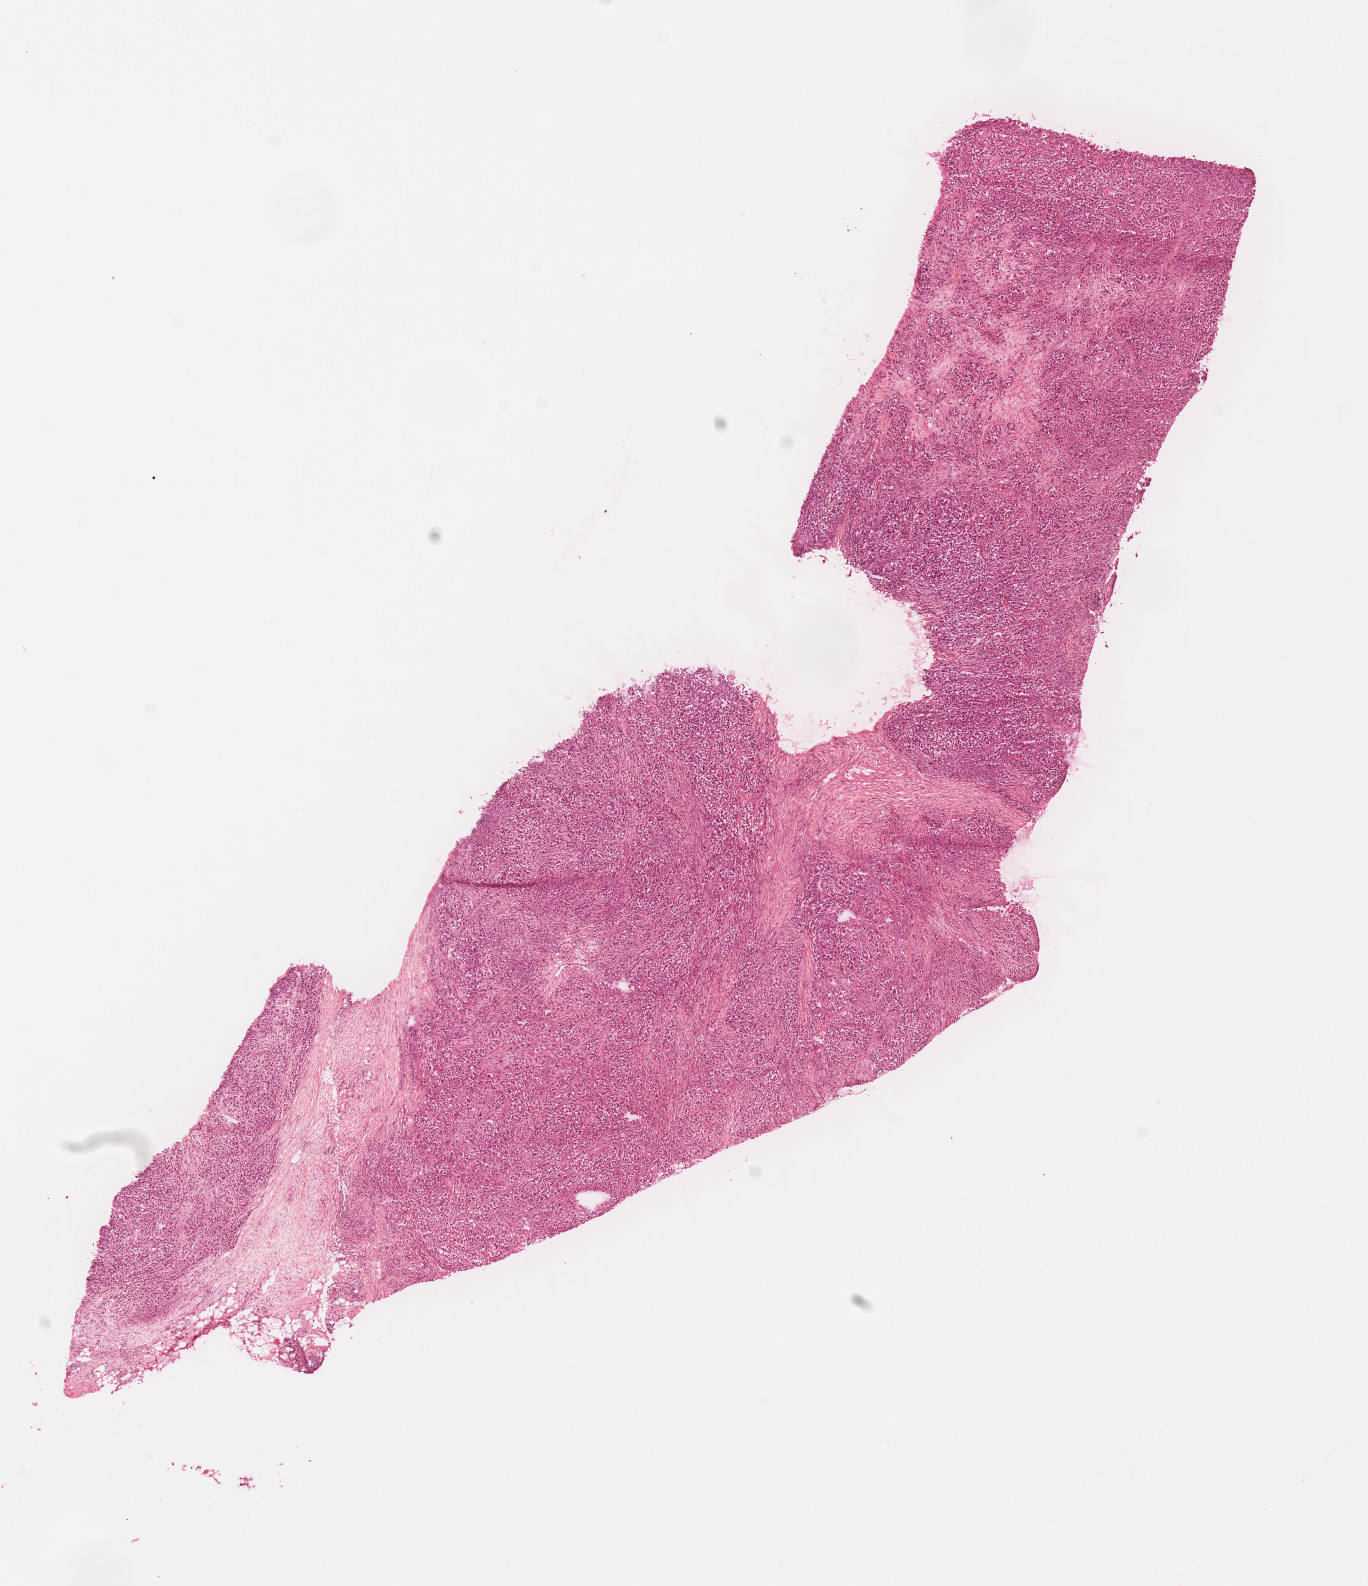
Whole-slide histology image, H&E, low-resolution overview of the scanned area, about 10.8 x 12.5 mm; FFPE section; primary tumour sample from the skin. Female, age 60 years at initial diagnosis.
Diagnosis: Malignant melanoma, NOS.